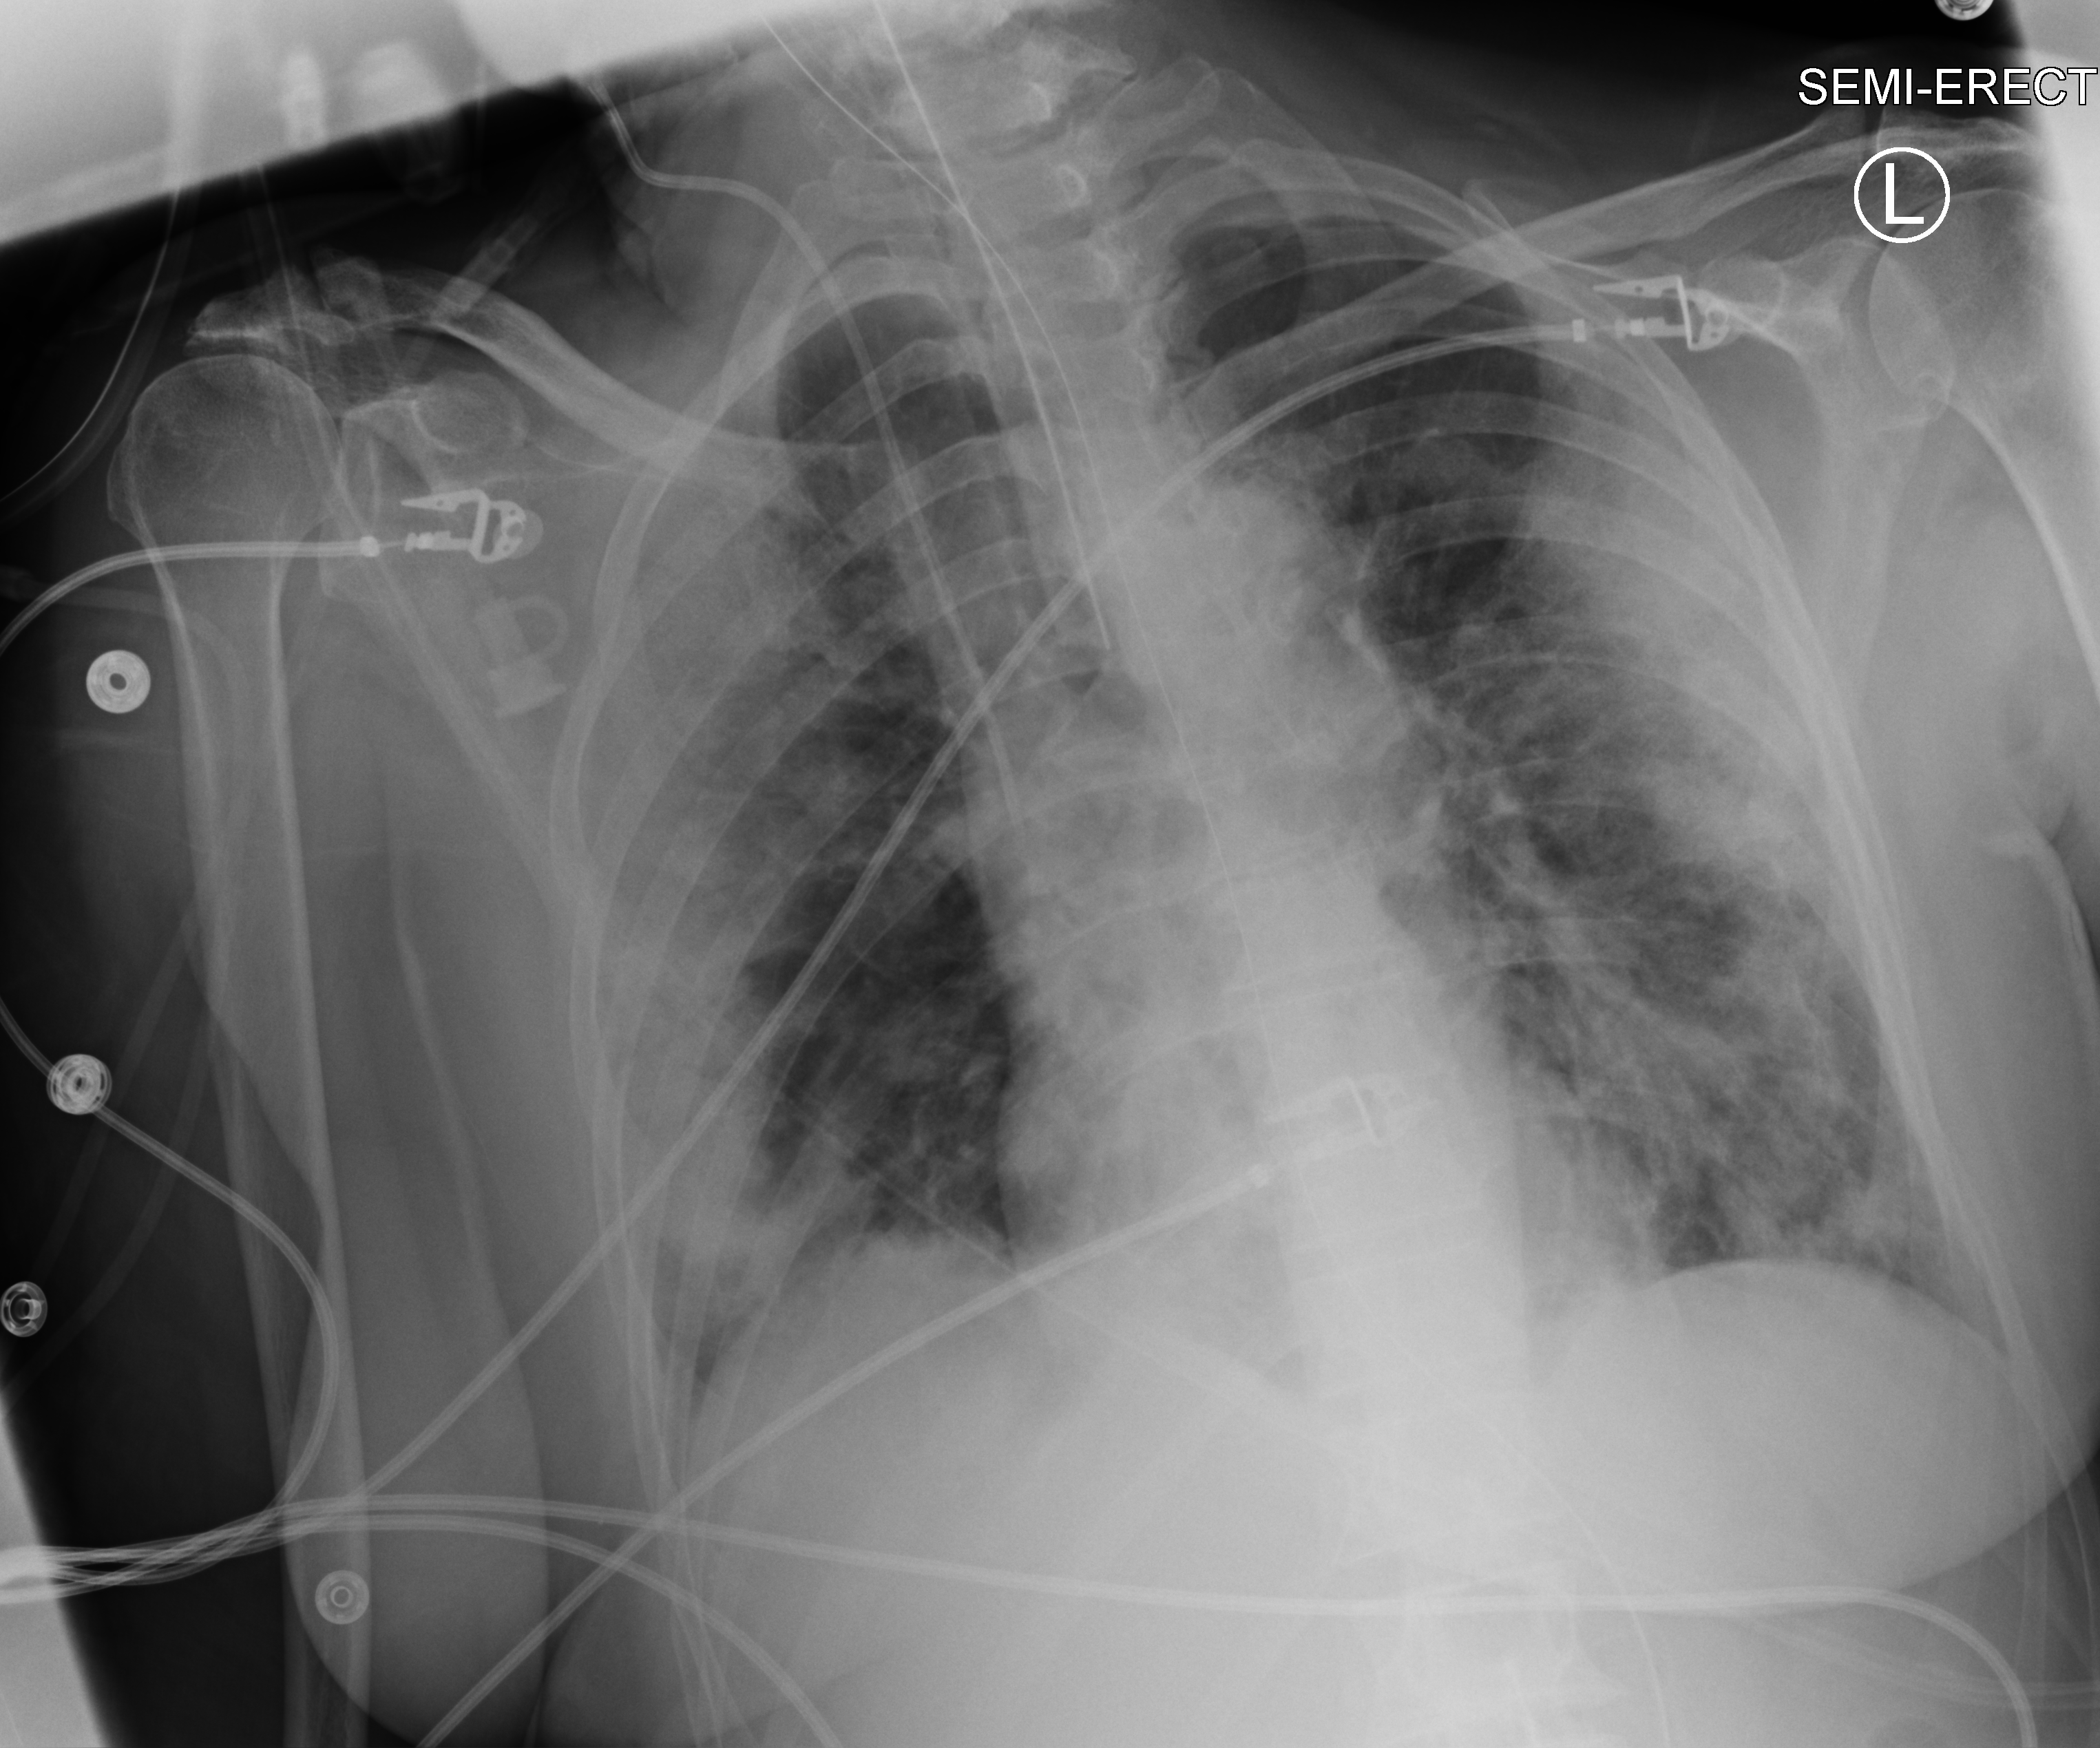
Portable chest radiograph; anteroposterior (AP) projection. Patient hospitalised with COVID-19; female, aged 60–74 years.
From the hospital-stay record, not from the radiograph (when in the stay this image was taken is not recorded):
- other chronic lung disease (admission record): no
- hypertension (admission record): yes